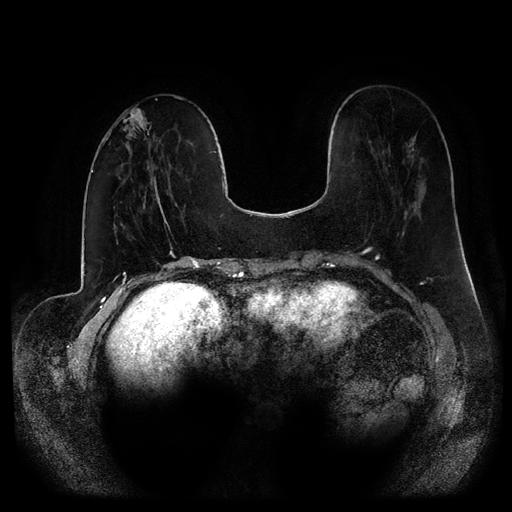
Breast MRI (dynamic contrast-enhanced, multi-phase), one axial slice; slice 31 of 116 in the series (ordered by position); dynamic contrast-enhanced series, time point 2 of 5 at this slice position (early post-contrast); 1.5 T; TE 2.6 ms, TR 5.2 ms; 2 mm slice thickness; 512 × 512 image matrix, field of view 380 × 380 mm. Patient: female, 53 years.
Annotated regions visible in this slice (semi-automatically segmented with operator editing):
- breast lesion (labelled 'tumour' in the annotation; benign lesions carry a separate 'benign' label): bounding box [x1, y1, x2, y2] px = [121, 107, 155, 152]